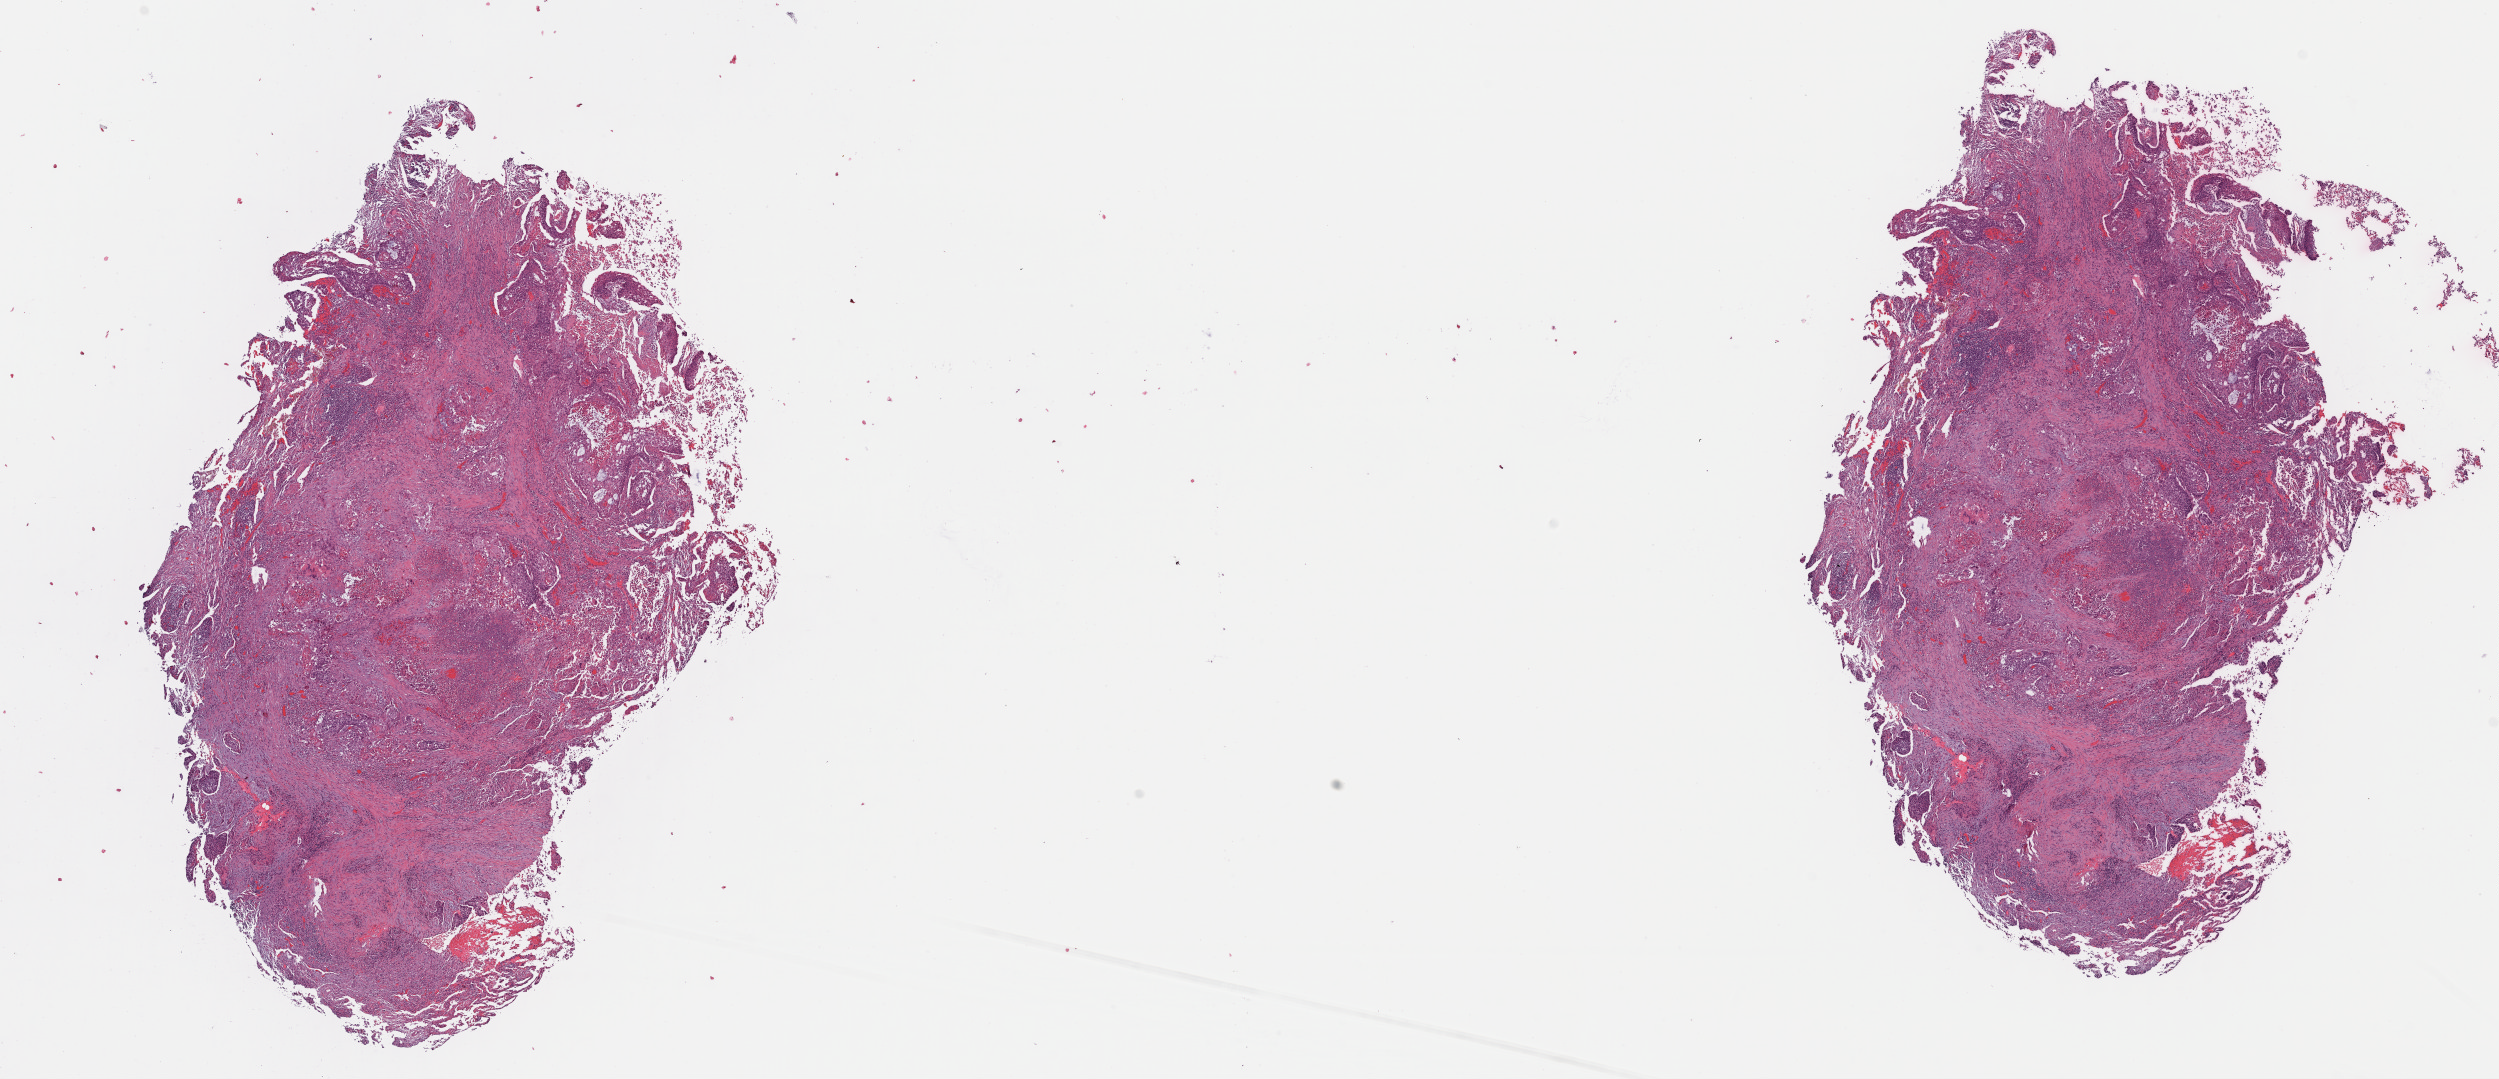
Whole-slide histology image, H&E, whole scanned area (about 19.6 x 8.5 mm, acquisition: 40x scan) shown as a low-resolution overview; formalin-fixed paraffin-embedded (FFPE) diagnostic section; sample: primary tumour, lung. Patient: female, age at initial diagnosis 76 years.
* TNM: T1a N0 M0
* AJCC pathologic stage: IA
* diagnosis: Squamous cell carcinoma, NOS (upper lobe, lung)